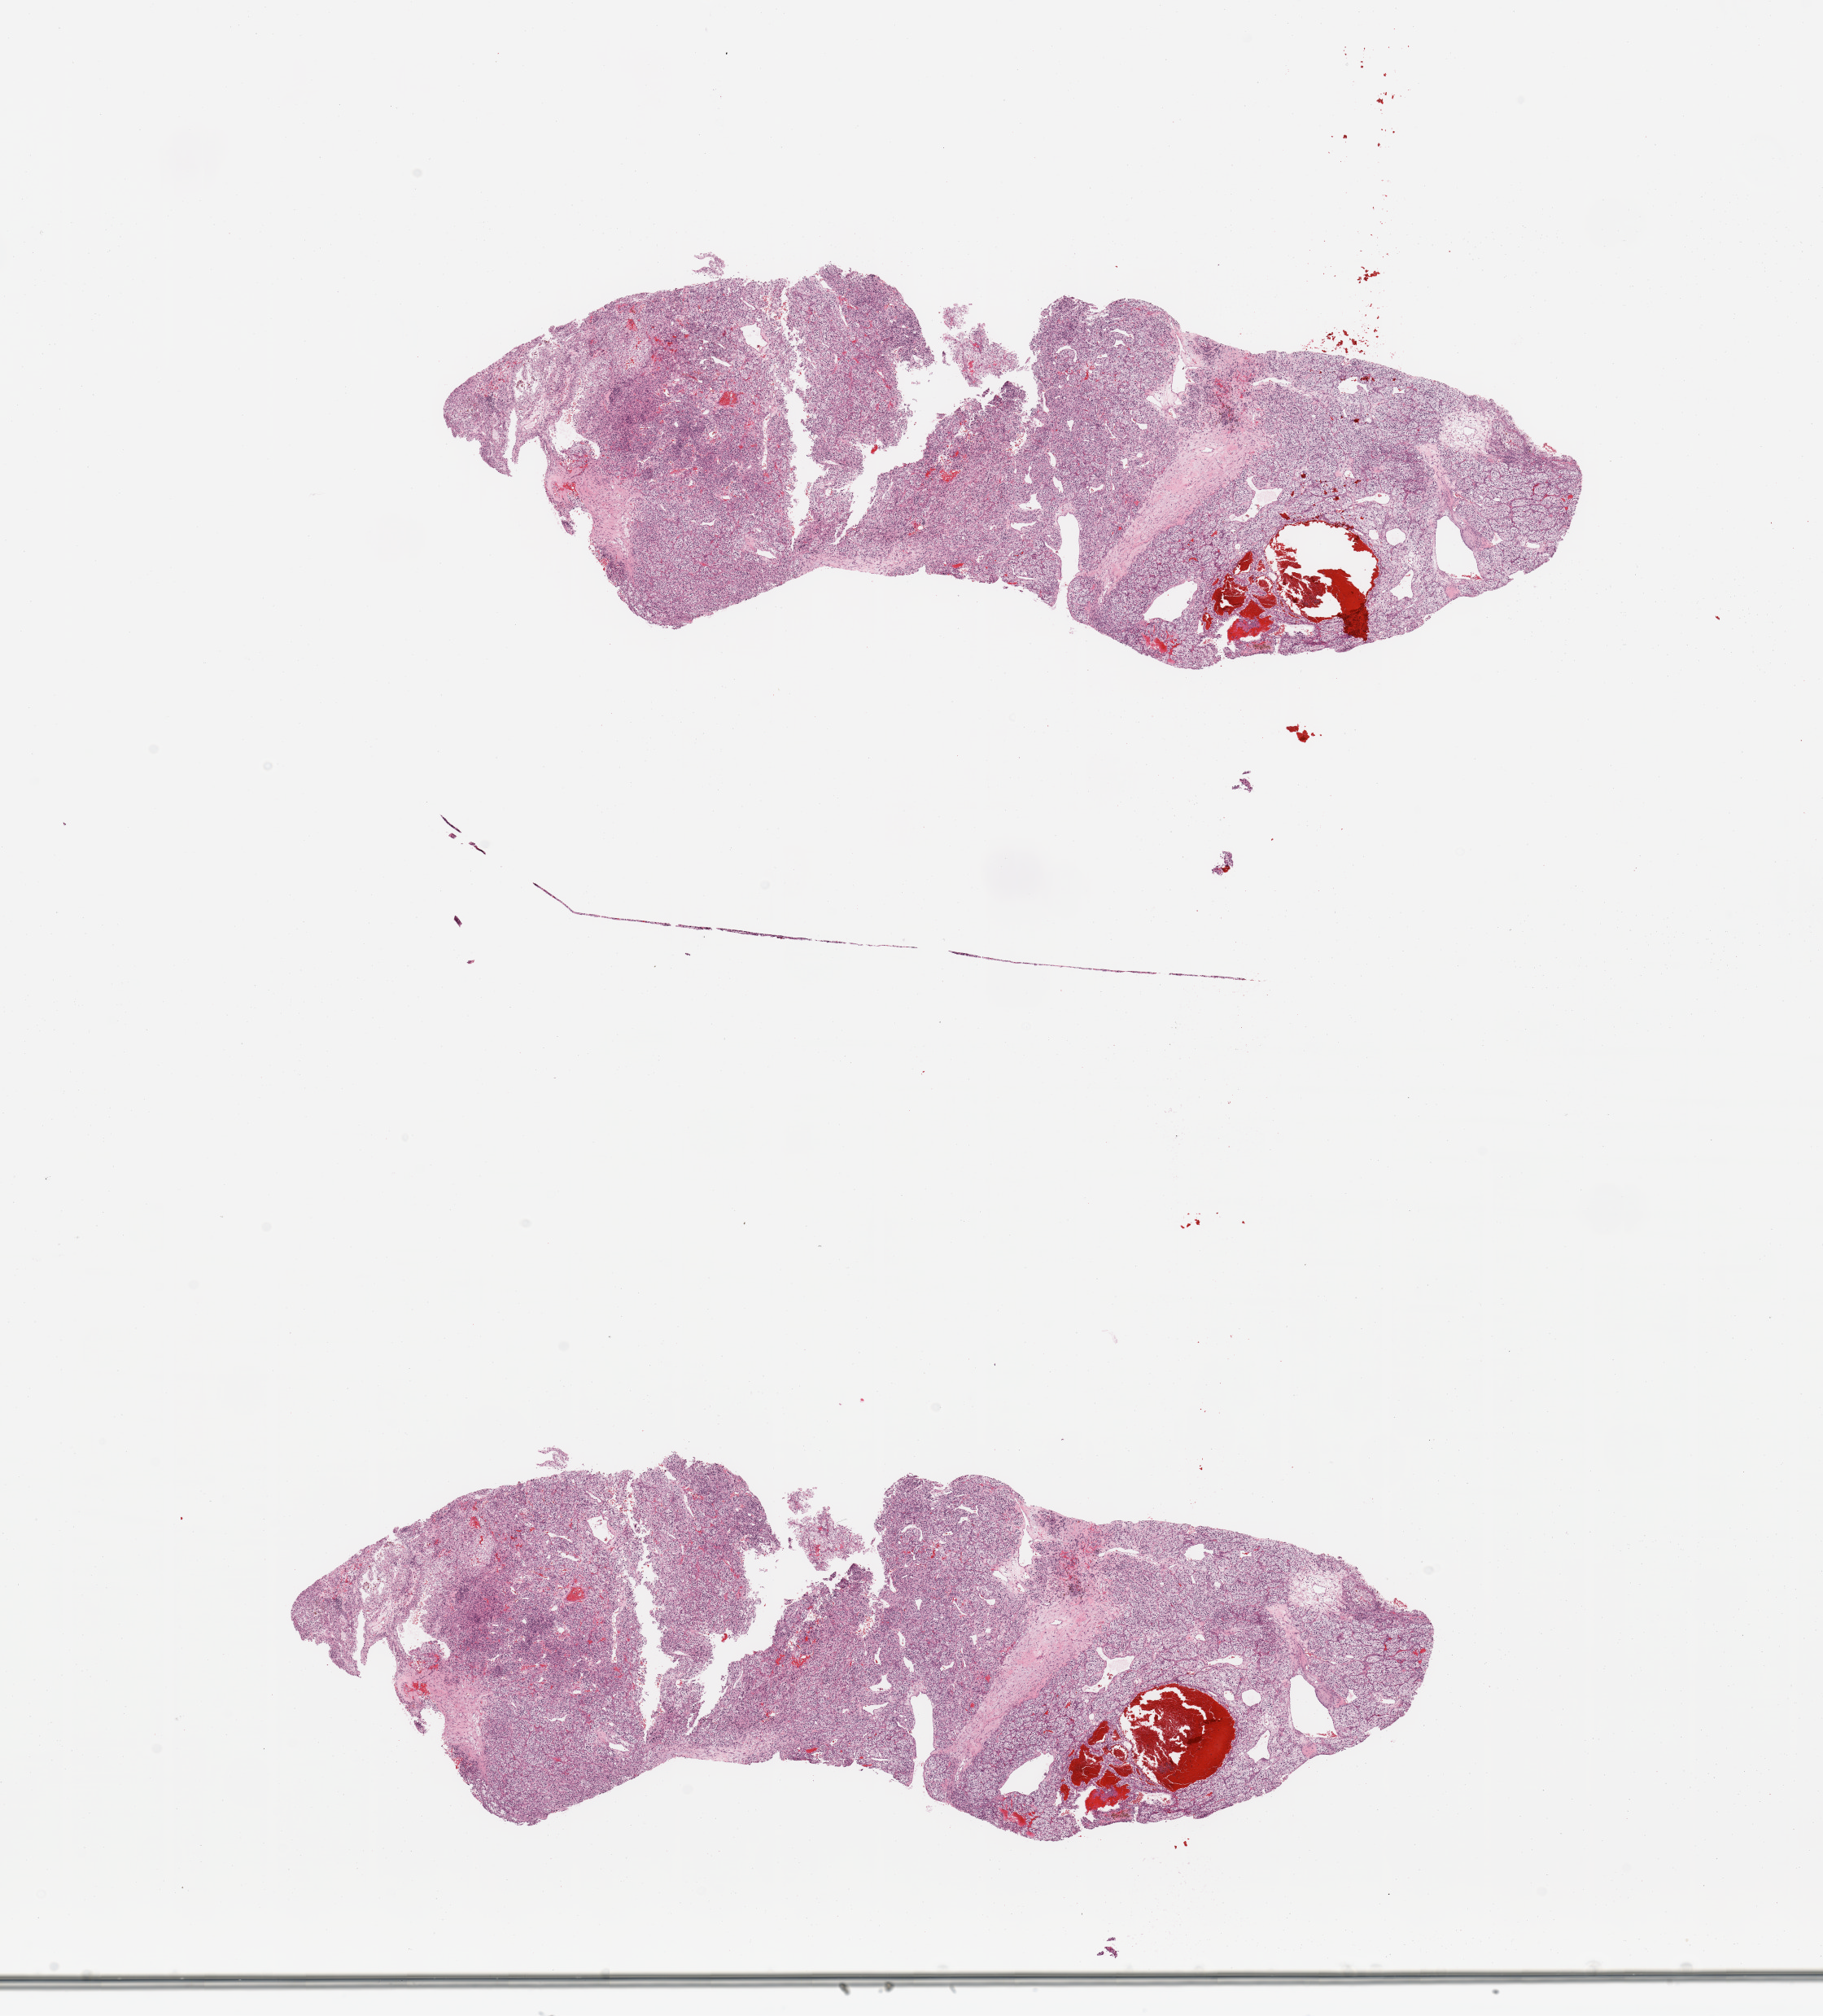
Whole-slide histology image, Hematoxylin and eosin (H&E) stained — shown as a low-resolution overview of the whole scanned area (about 17.7 x 19.6 mm); tumour tissue sample, sampled site: kidney. 83-year-old male patient. Histologic grade: G3 (poorly differentiated). Pathologist review of this section (percent, as recorded): tumour nuclei 85%, necrosis 5%.
• diagnosis: Renal cell carcinoma, NOS
• AJCC pathologic stage: III
• primary tumour site (as recorded): lower pole